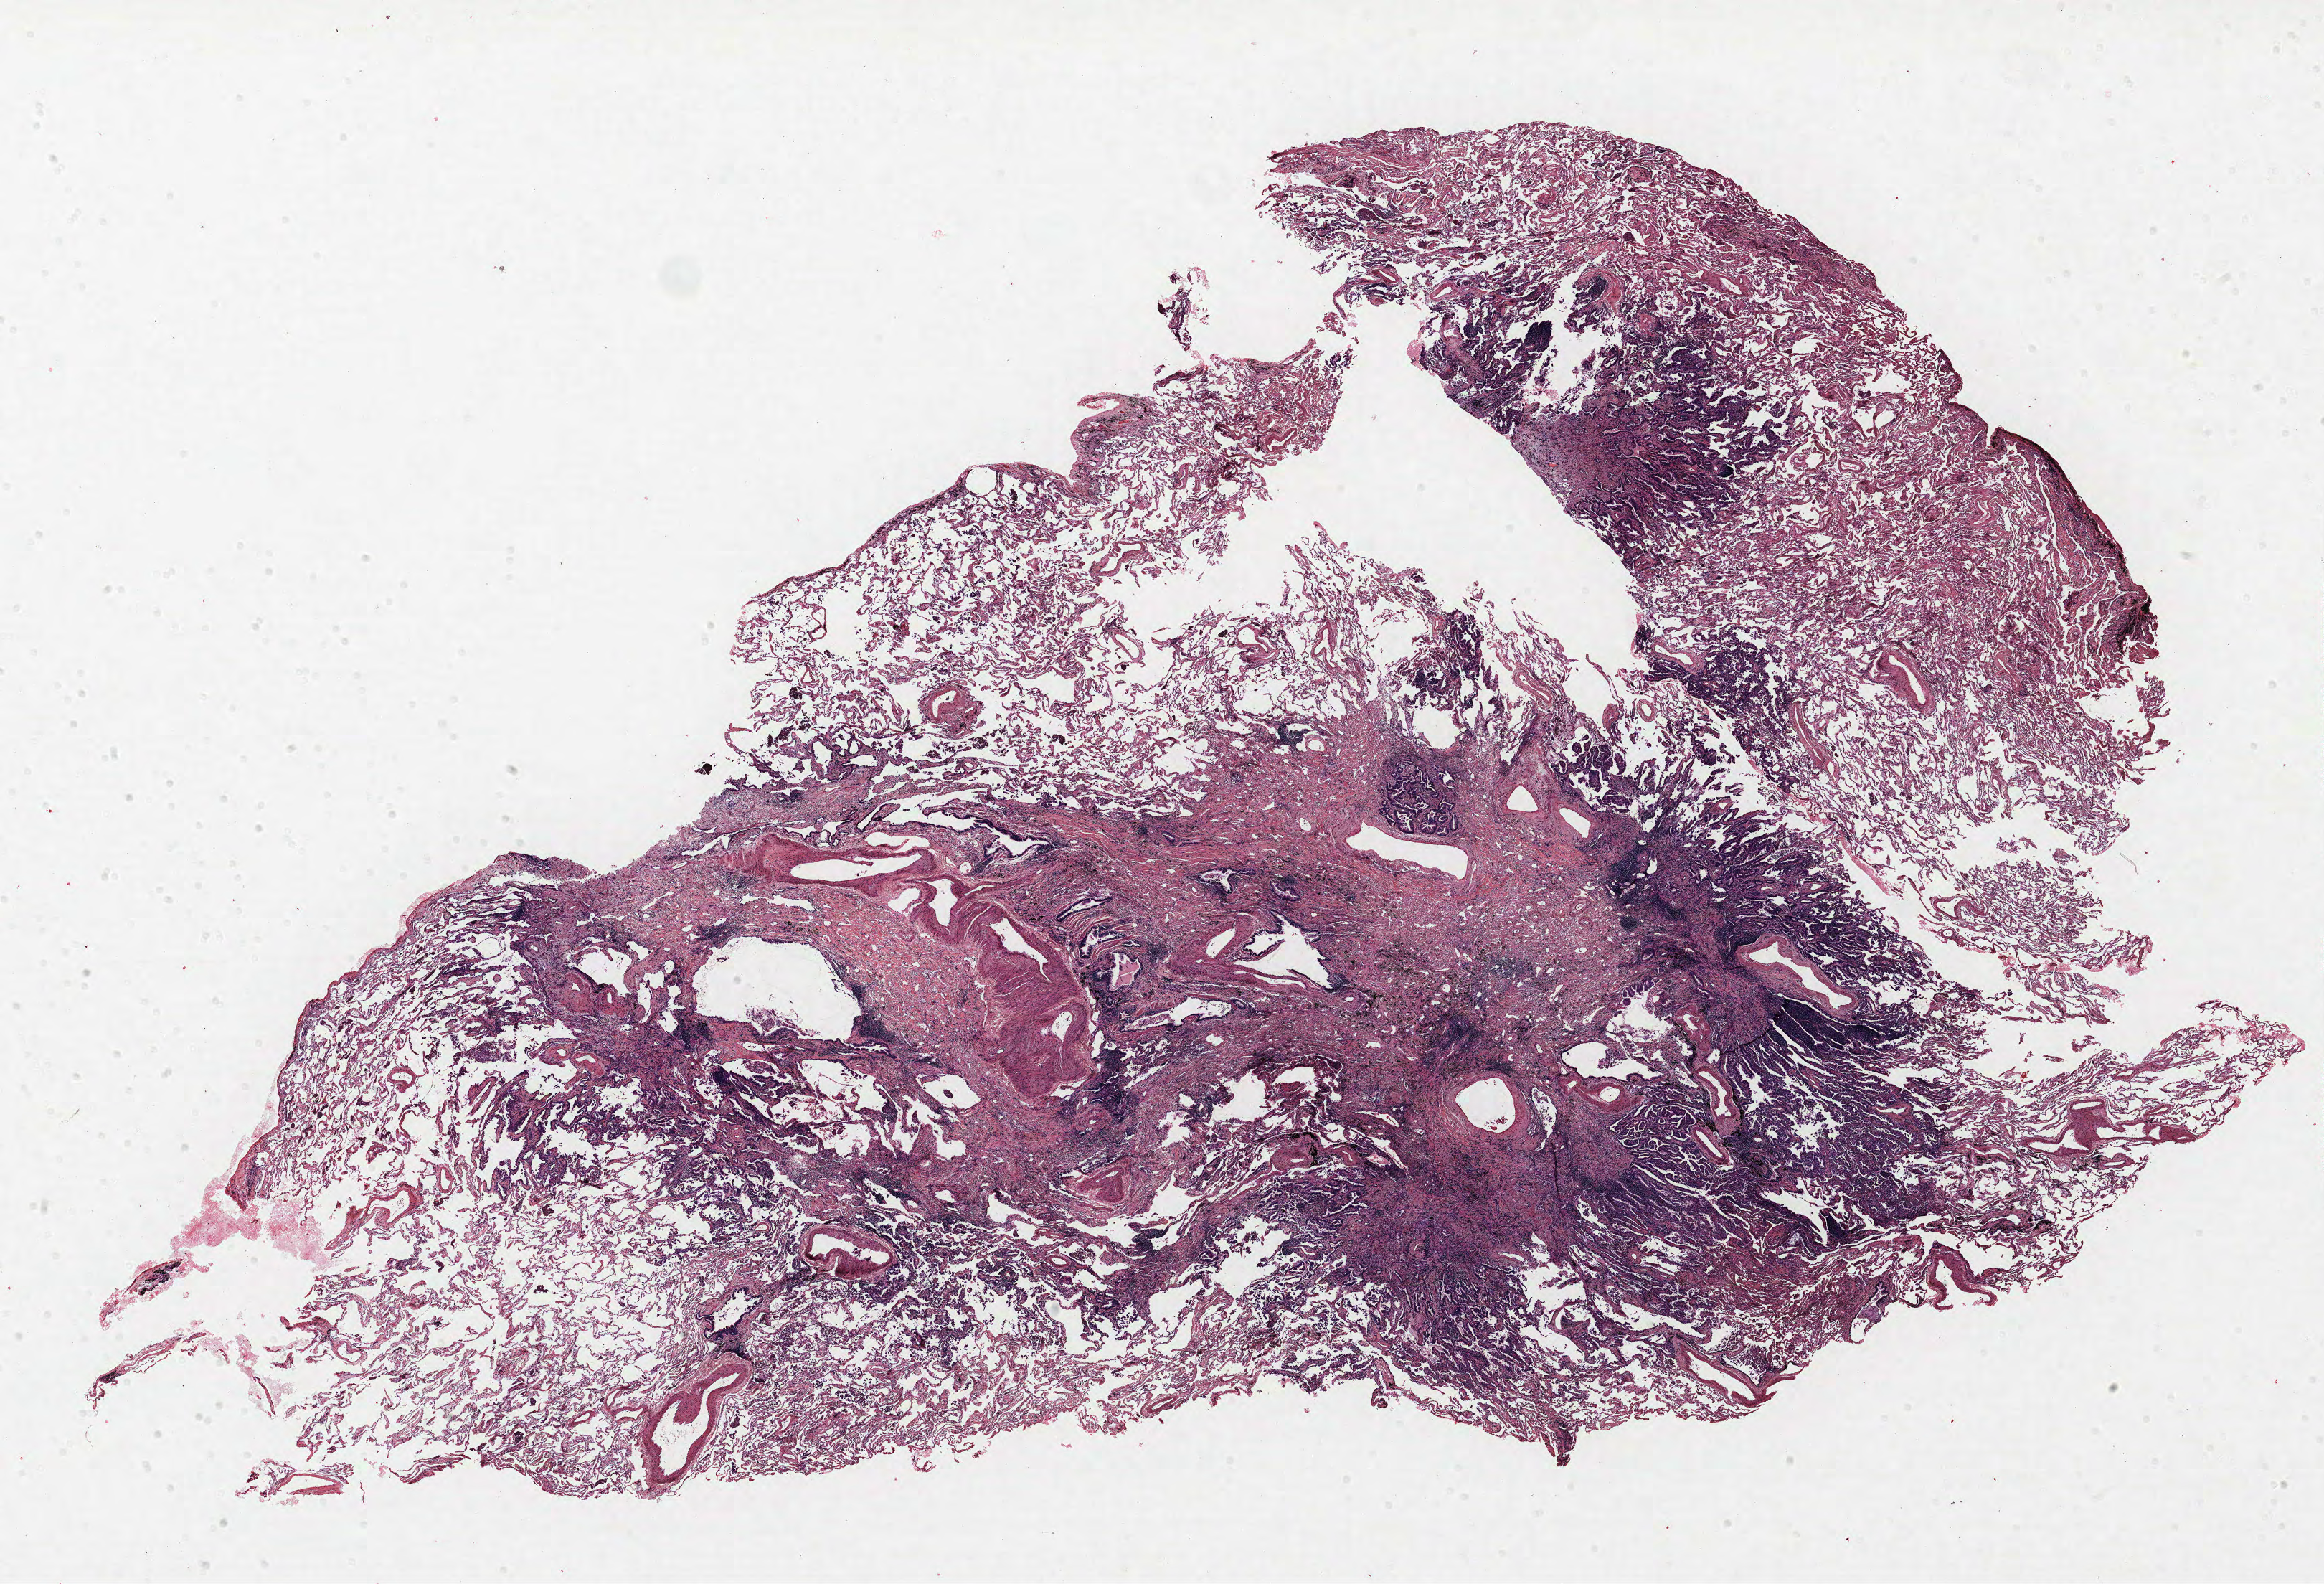
Hematoxylin and eosin (H&E) stained whole-slide image — whole scanned area (about 25.9 x 17.7 mm, from a 40x scan) shown as a low-resolution overview, formalin-fixed paraffin-embedded (FFPE) section, lung tissue. Male patient, aged 69 at enrolment. Grade: moderately differentiated (G2).
• tumour size (pathology): 10 mm
• participant's lung-cancer diagnosis: Adenocarcinoma with mixed subtypes (ICD-O-3 8255/3)
• stage (AJCC 6th edition): IA
• primary tumour location (clinical record): left upper lobe
• ICD-O-3 topography: upper lobe of lung (C34.1)